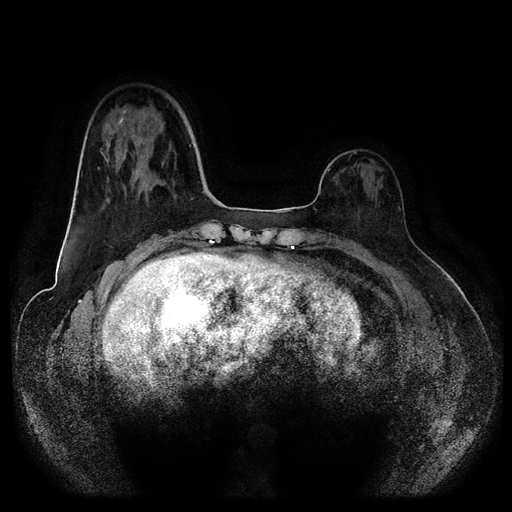
Breast MRI (dynamic contrast-enhanced, multi-phase), one axial slice; slice 31 of 116 in the series (ordered by position); dynamic contrast-enhanced series, time point 2 of 5 at this slice position (early post-contrast); 1.5 T; TE 2.6 ms, TR 5.2 ms; 2 mm slice thickness; 512 × 512 image matrix, field of view 380 × 380 mm. Patient: female, 50 years.
Annotated regions visible in this slice (semi-automatic segmentation, software-assisted and operator-edited):
- breast lesion (labelled benign in the annotation): bounding box <132,137,153,181> (left, top, right, bottom; pixels)